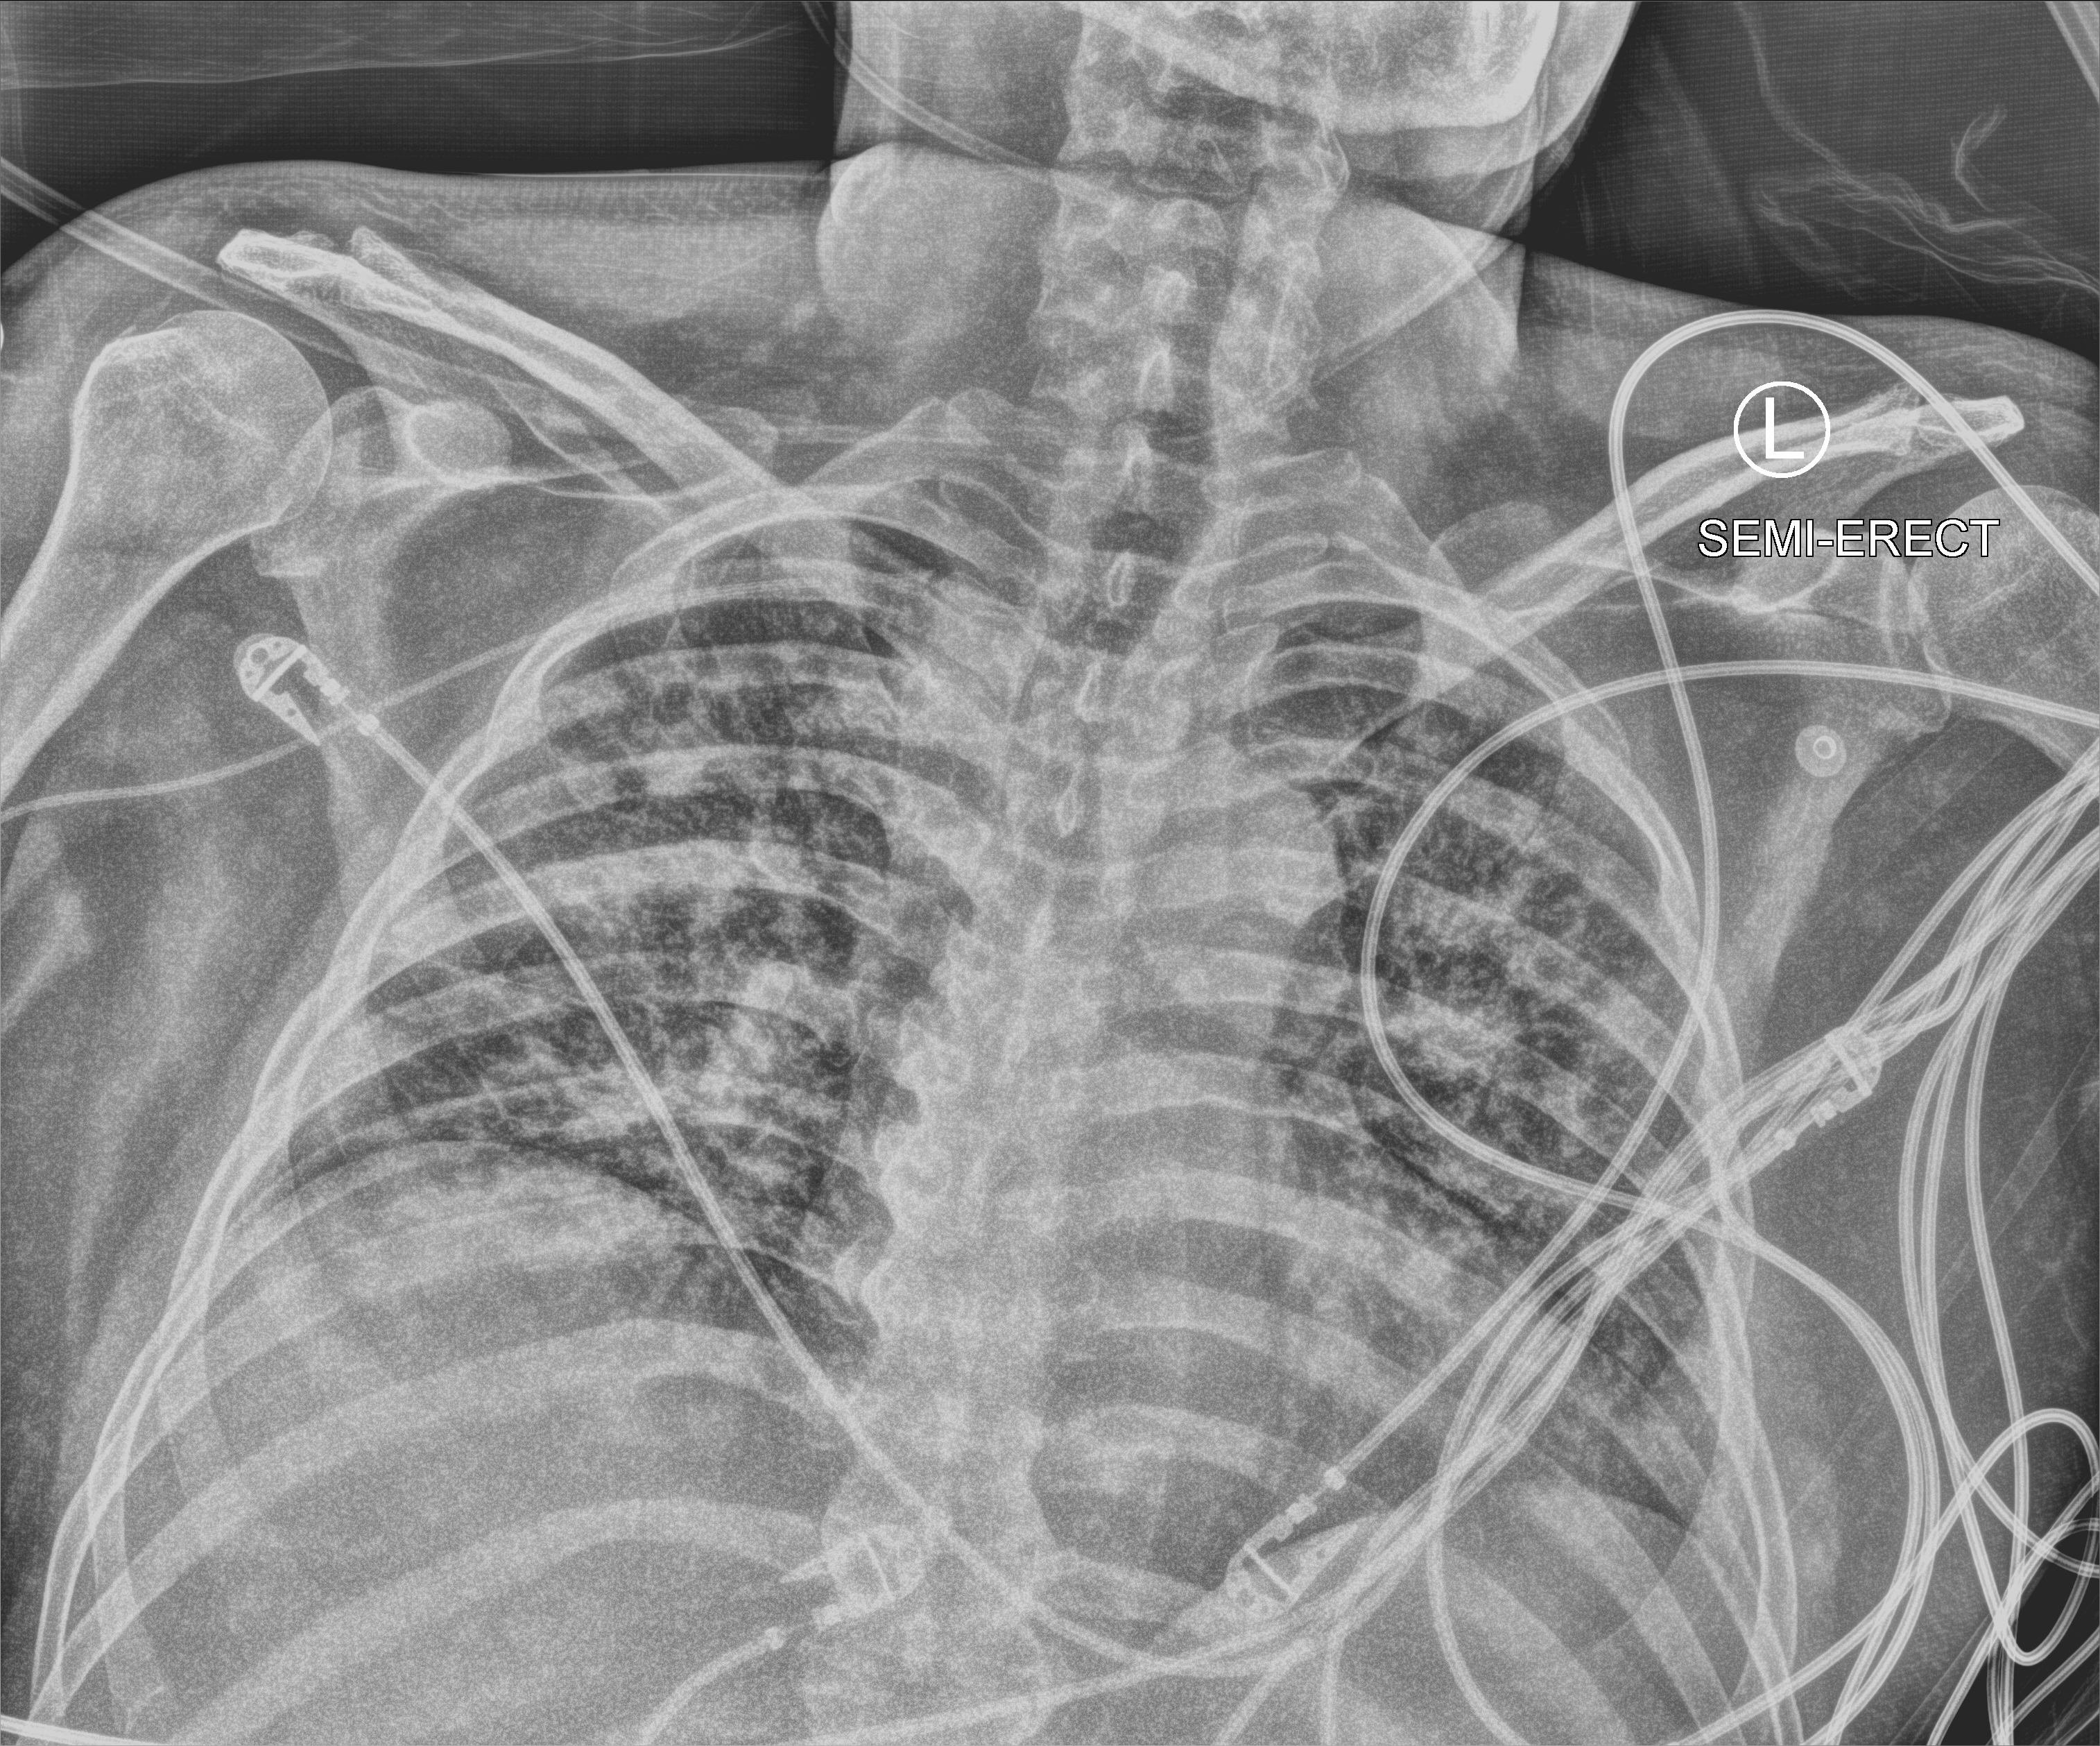
Portable chest radiograph; anteroposterior (AP) projection. Patient hospitalised with COVID-19; male, aged 18–59 years.
Hospital-stay facts (about this admission, not read from this image; timing relative to this image not recorded): mechanically ventilated during this hospital stay: yes; COPD (admission record): no; chronic kidney disease (admission record): no.